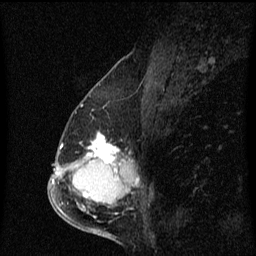
Breast MRI (dynamic contrast-enhanced), one sagittal slice; position 31 of 60 along the scan axis; dynamic contrast-enhanced series, image 2 of 3 at this slice position (ordered by acquisition); 1.5 T; TE 4.2 ms, TR 8.4 ms; 2 mm slice thickness; 256 × 256 image matrix, field of view 200 × 200 mm. Patient: female, 57 years. Case-level facts recorded for this patient, not image findings: setting: breast cancer imaged before/during neoadjuvant chemotherapy; receptor status: HR-positive, HER2-negative.
Outlined on this slice (semi-automatic segmentation, software-assisted and operator-edited):
- analysis volume of interest (the breast-tissue region the enhancement analysis was run in; not a lesion): bounding box <66,128,129,177> (left, top, right, bottom; pixels)
- tumour enhancement mask (voxels above the 70 % enhancement threshold inside the analysis volume of interest): <86,134,117,173>